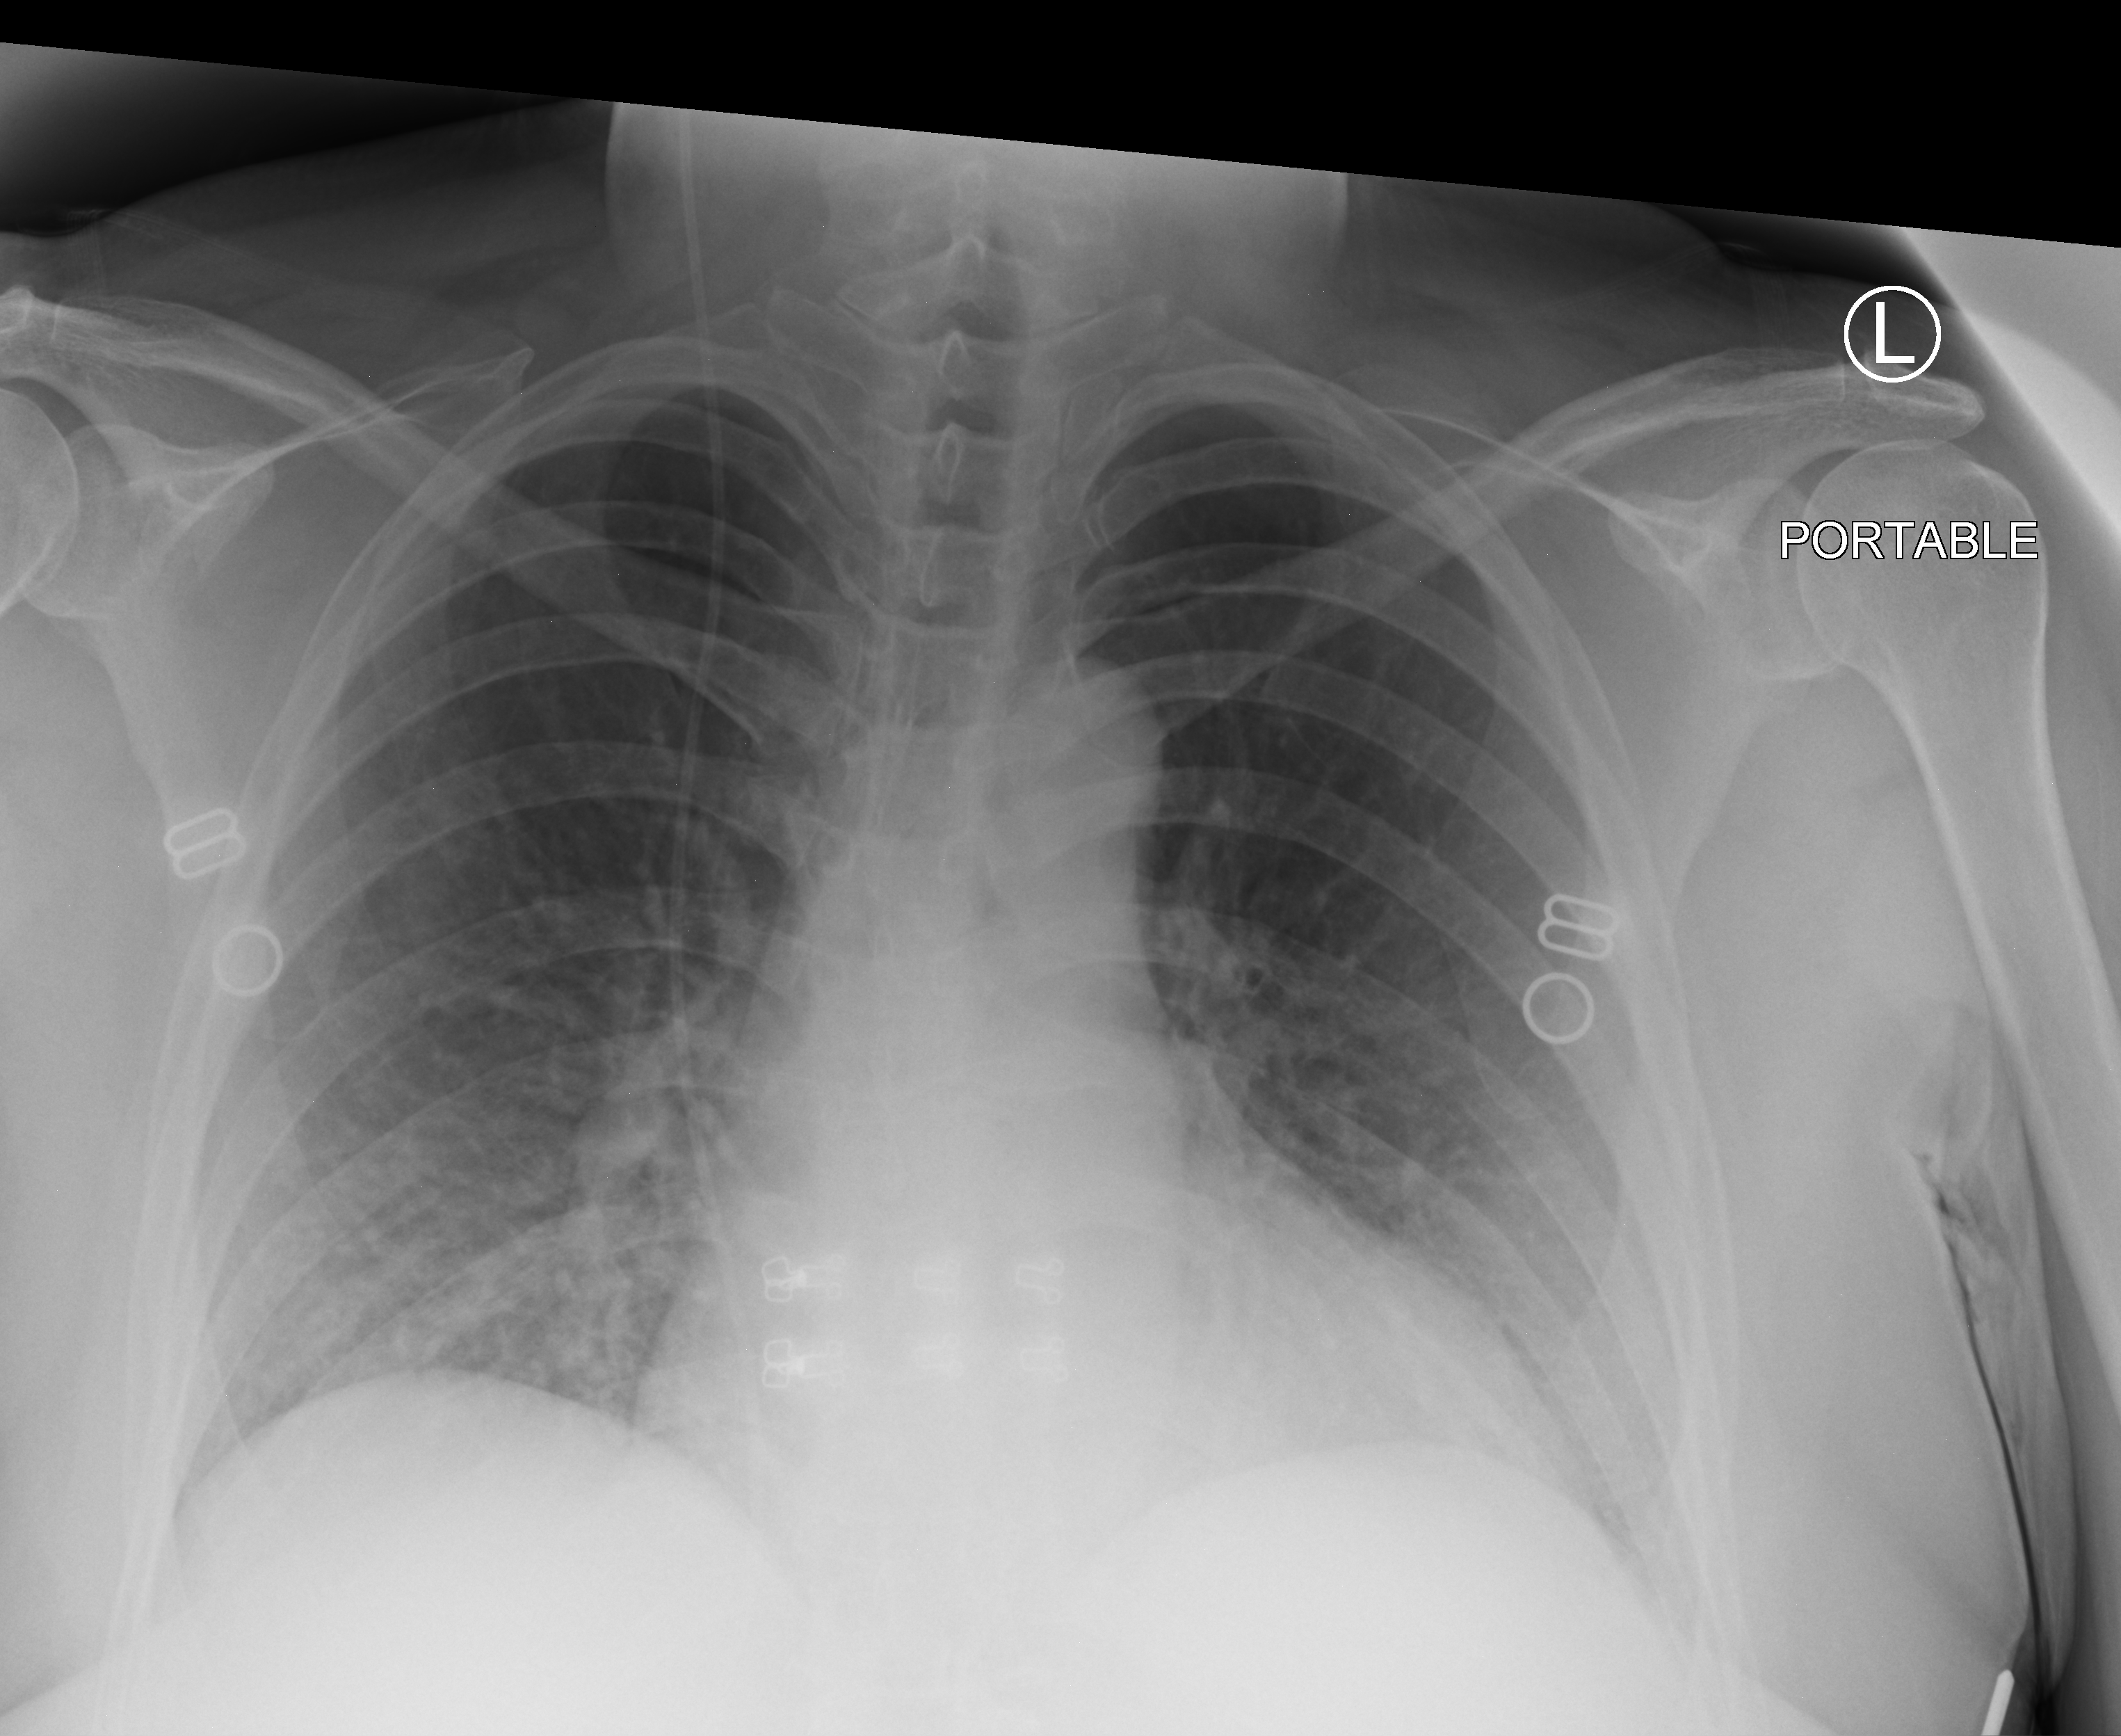
Bedside chest radiograph (computed radiography); anteroposterior (AP) projection. Patient hospitalised with COVID-19; female, aged 18–59 years.
From the hospital-stay record, not from the radiograph (when in the stay this image was taken is not recorded):
- diabetes (admission record): no
- mechanically ventilated during this hospital stay: no